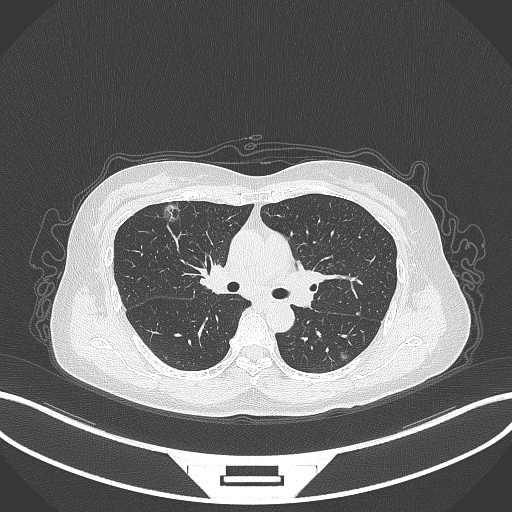
Chest CT, one axial slice; slice 200 of 315 in the series (ordered by position); reconstruction kernel B70f; 120 kVp; lung window (W 1500 / L -600 HU); 1 mm slice thickness; 512 × 512 image matrix, field of view 400 × 400 mm. Patient: female, 61 years. Case-level facts recorded for this patient, not image findings: clinical TNM (as recorded): T1b N0 M0; histopathological grade: G1.
Structures marked on this image (rectangle marked by the reading radiologist):
- lung tumour (recorded histology: adenocarcinoma): bounding box (x1, y1, x2, y2) in pixels: (158, 203, 185, 227)